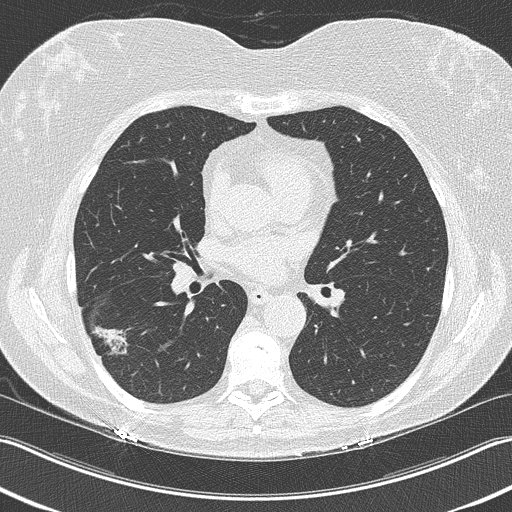
Low-dose screening chest CT, one axial slice. Position 119 of 210 along the scan axis. Reconstruction kernel B50f. Lung window (W 1500 / L -600 HU). 2 mm slice thickness. 512 × 512 image matrix.
Outlined on this slice (expert manual segmentation):
- lesion 1 (tumor, lower lobe of right lung): bounding box [x1, y1, x2, y2] px = [92, 326, 131, 355]